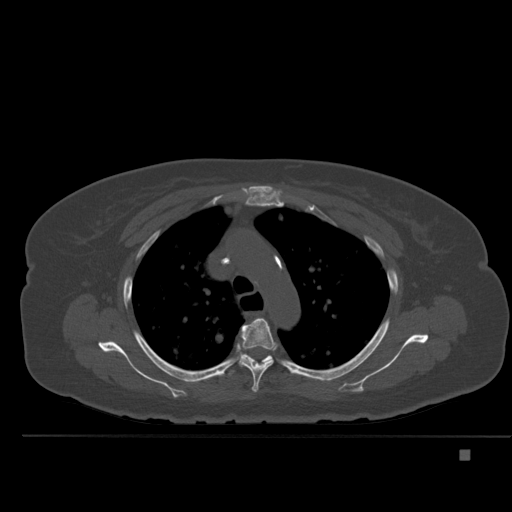
CT including the spine, one axial slice; position 363 of 477 along the scan axis; bone window (W 1800 / L 400 HU); 1.5 mm slice thickness; 512 × 512 image matrix. Patient: female, 74 years. Case-level facts recorded for this patient, not image findings: primary cancer: colon.
Structures marked on this image (semi-automatically segmented with operator editing):
- T4 vertebra: box from (x=239, y=318) to (x=278, y=392) px
- T5 vertebra: (x=229, y=354)–(x=273, y=376)